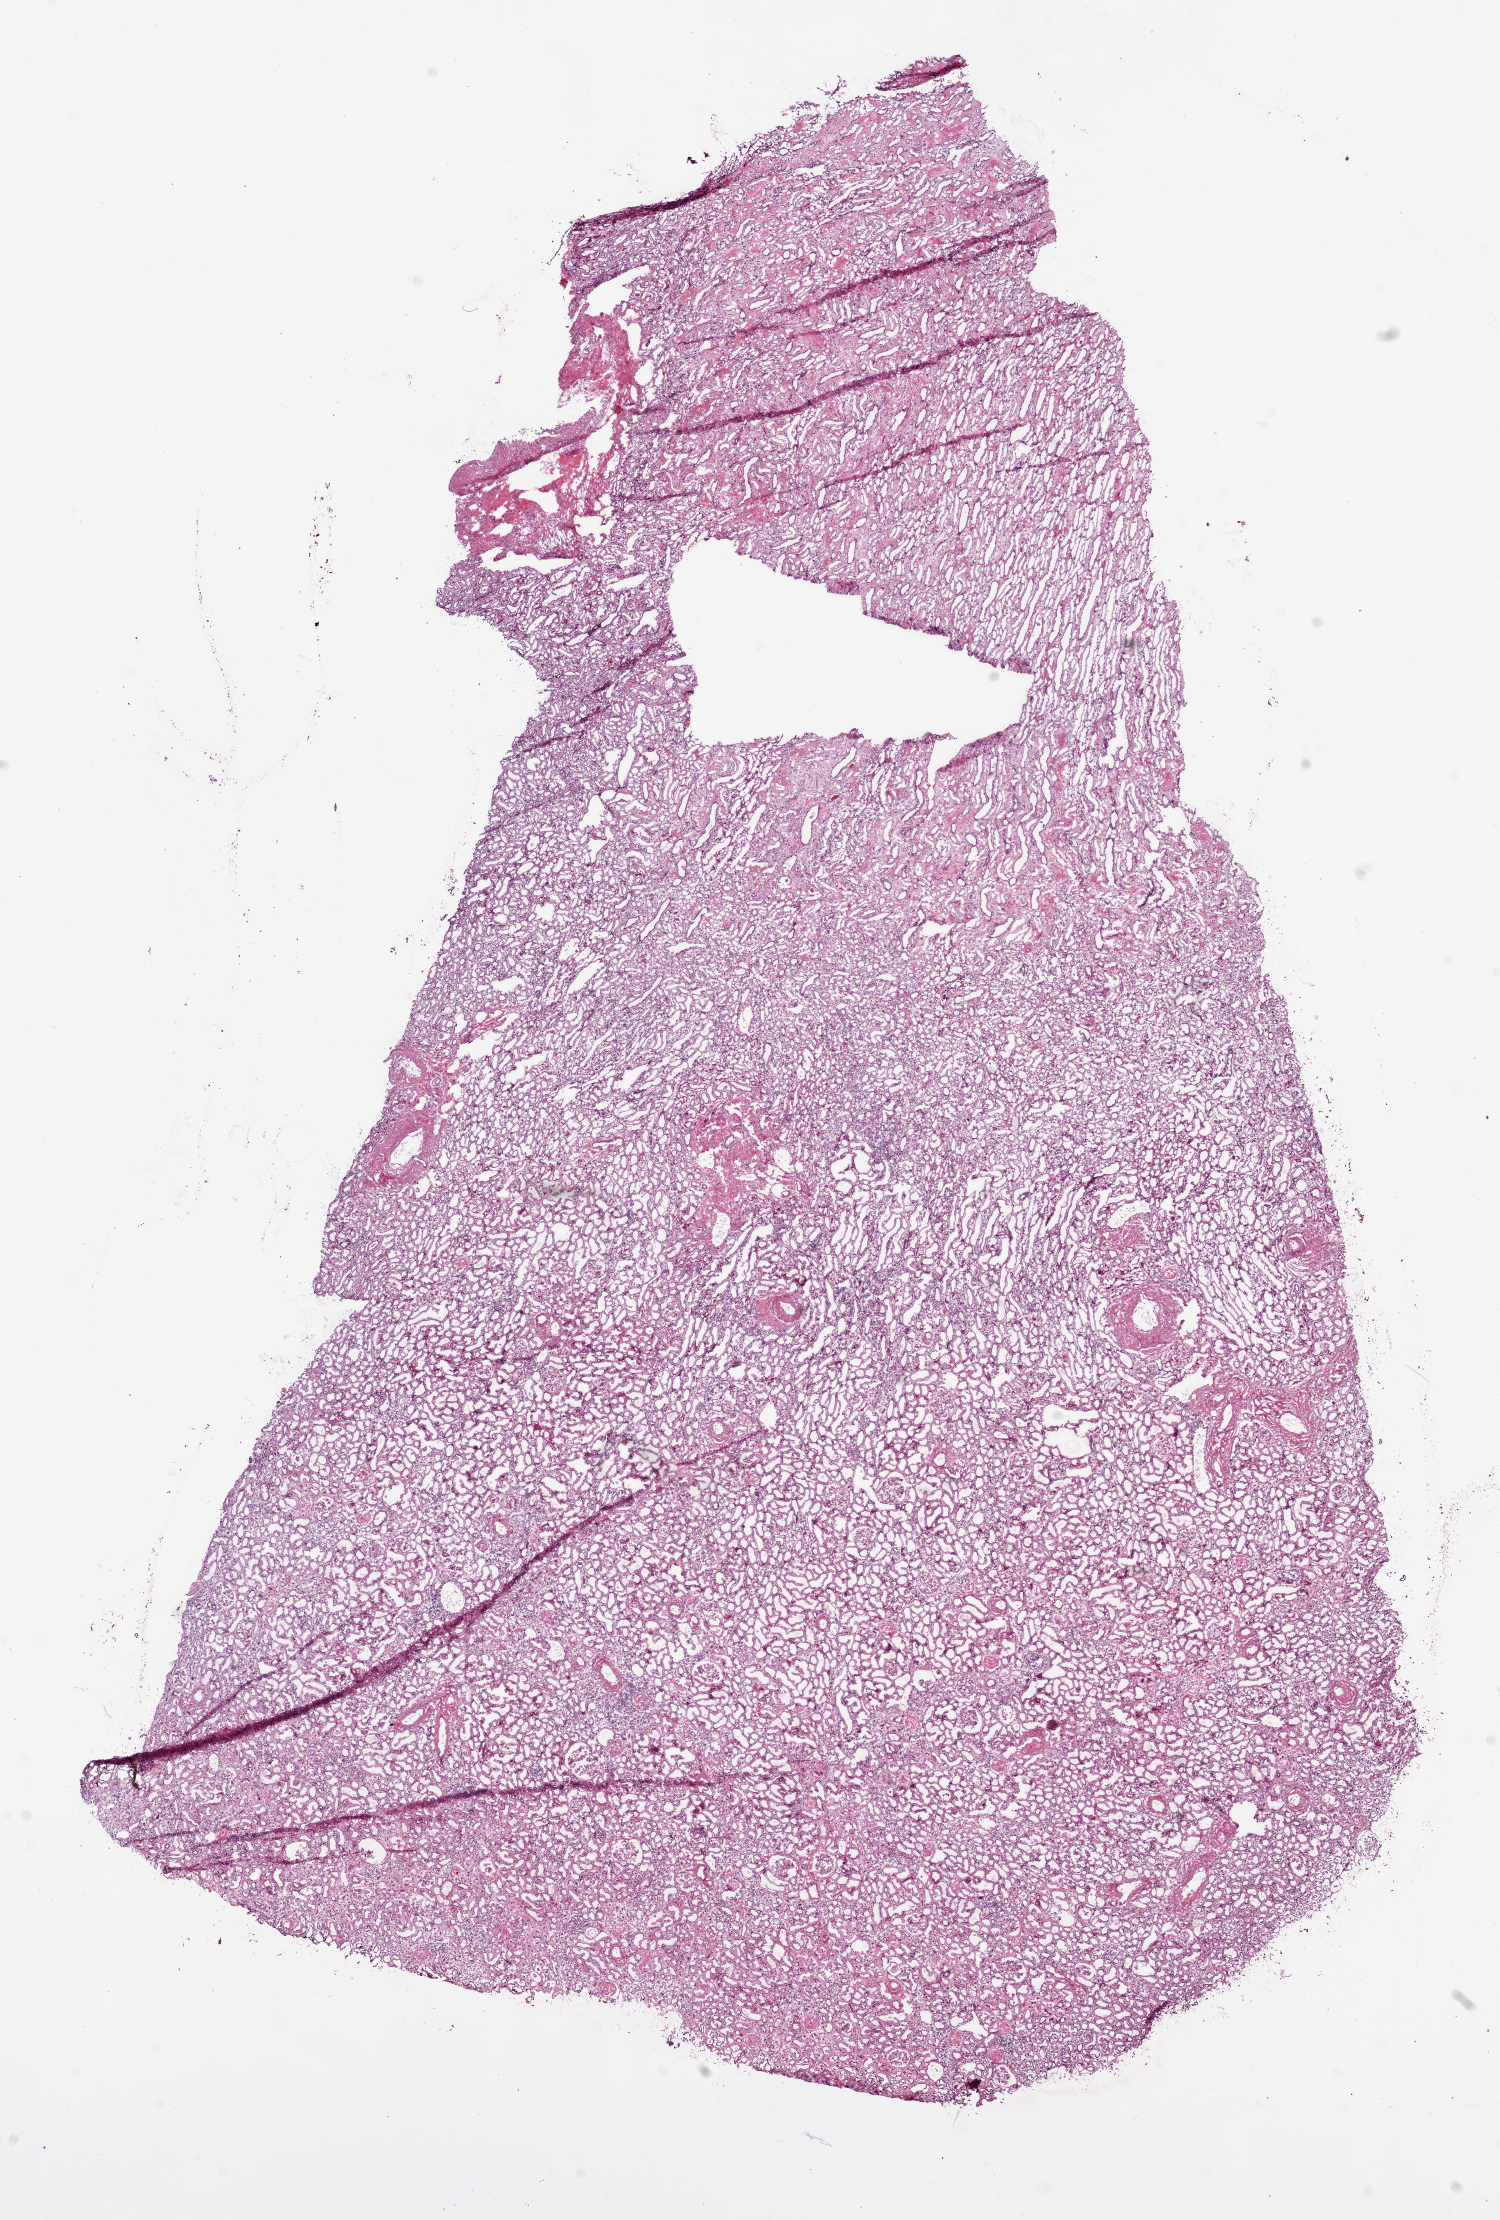
Digitized H&E-stained tissue section (whole slide), whole scanned area (about 12.0 x 17.8 mm) shown as a low-resolution overview. Frozen section from the bottom of the tissue portion. Kidney, solid tissue normal (non-tumour tissue) sample. Male patient; age at initial diagnosis 88 years.
* this section: solid tissue normal (non-tumour) sample from the same patient
* patient diagnosis: Clear cell adenocarcinoma, NOS